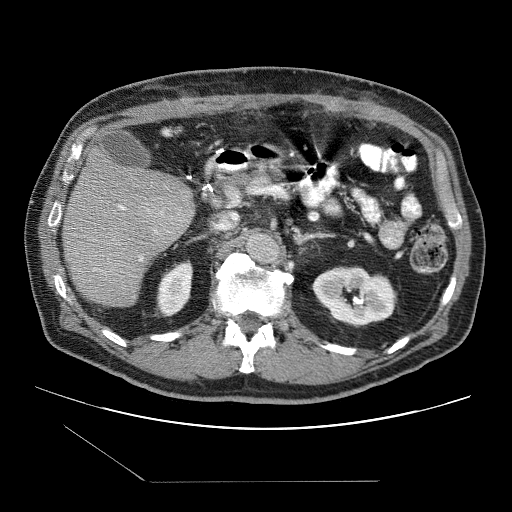
Contrast-enhanced abdominal CT (liver protocol), one axial slice. Position 45 of 109 along the scan axis. Reconstruction kernel STANDARD. 120 kVp. One of 2 acquisitions stored at this slice position. Soft-tissue window (W 400 / L 40 HU). 512 × 512 image matrix. Case-level facts recorded for this patient, not image findings: diagnosis: hepatocellular carcinoma (patient treated with transarterial chemoembolisation; whether this scan precedes or follows treatment is not stated here); TNM stage (as recorded): Stage-IIIB; Child-Pugh class: A; tumour differentiation: well differentiated; tumour nodularity: multinodular.
Outlined on this slice (semi-automatically segmented with operator editing):
- liver parenchyma outside the tumour (the mass and vessels are separate outlines, so this box may not span the whole liver): bounding box <62,148,194,306> (left, top, right, bottom; pixels)
- liver vessels: <94,205,168,270>